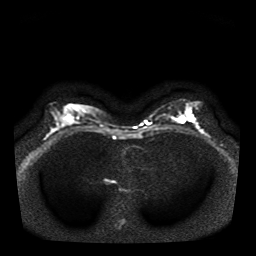
Breast MRI, one axial slice; slice 21 of 41 in the series (ordered by position); diffusion-weighted series; image 2 of 4 stored at this slice position (different b-values; order by instance number); 1.5 T; 256 × 256 image matrix, field of view 330 × 330 mm. Female patient.
Structures marked on this image (expert manual segmentation):
- tumour on diffusion-weighted imaging: bounding box (x1, y1, x2, y2) in pixels: (186, 113, 194, 121)